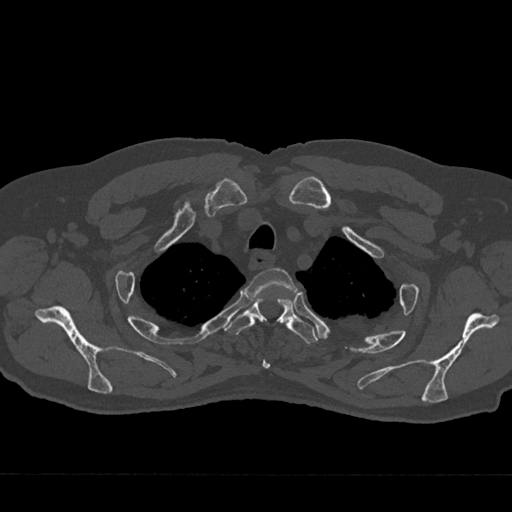
CT including the spine, one axial slice; slice 585 of 797 in the series (ordered by position); reconstruction kernel Br40s/3; bone window (W 1800 / L 400 HU); 0.5 mm slice thickness; 512 × 512 image matrix, field of view 377 × 377 mm. Male patient, age 75 years. From the clinical record (not read from this slice): primary cancer: renal; vertebrae with lytic lesions (as recorded): T4.
Structures marked on this image (semi-automatic segmentation, software-assisted and operator-edited):
- T2 vertebra: bounding box <248,268,297,369> (left, top, right, bottom; pixels)
- T3 vertebra: <226,297,318,344>